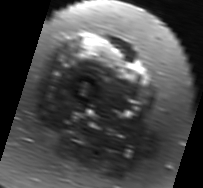
MRI of an extremity soft-tissue mass, one axial slice; slice 19 of 91 in the series (ordered by position); T2-weighted fat-saturated; MR volume resampled by the dataset authors to the PET/CT grid (not the native acquisition matrix); 3.27 mm slice thickness; 203 × 188 image matrix, field of view 198 × 184 mm. Female patient. Case-level facts recorded for this patient, not image findings: histological type: malignant solitary fibrous tumor; grade: intermediate; site of the primary tumour: right thigh.
Outlined on this slice (expert contour drawn on MRI and transferred to this co-registered scan by the dataset authors):
- gross tumour volume including surrounding oedema: bounding box (x1, y1, x2, y2) in pixels: (78, 35, 139, 80)